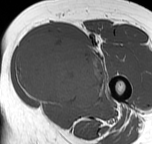
MRI of an extremity soft-tissue mass, one axial slice. Slice 30 of 57 in the series (ordered by position). MR volume resampled by the dataset authors to the PET/CT grid (not the native acquisition matrix). 3.27 mm slice thickness. 152 × 144 image matrix. Female patient. Case-level facts recorded for this patient, not image findings: histological type: pleiomorphic leiomyosarcoma; grade: intermediate; site of the primary tumour: left thigh.
Outlined on this slice (expert contour drawn on MRI and transferred to this co-registered scan by the dataset authors):
- gross tumour volume including surrounding oedema: bounding box [x1, y1, x2, y2] px = [15, 35, 105, 109]
- gross tumour volume (mass): [15, 37, 105, 107]